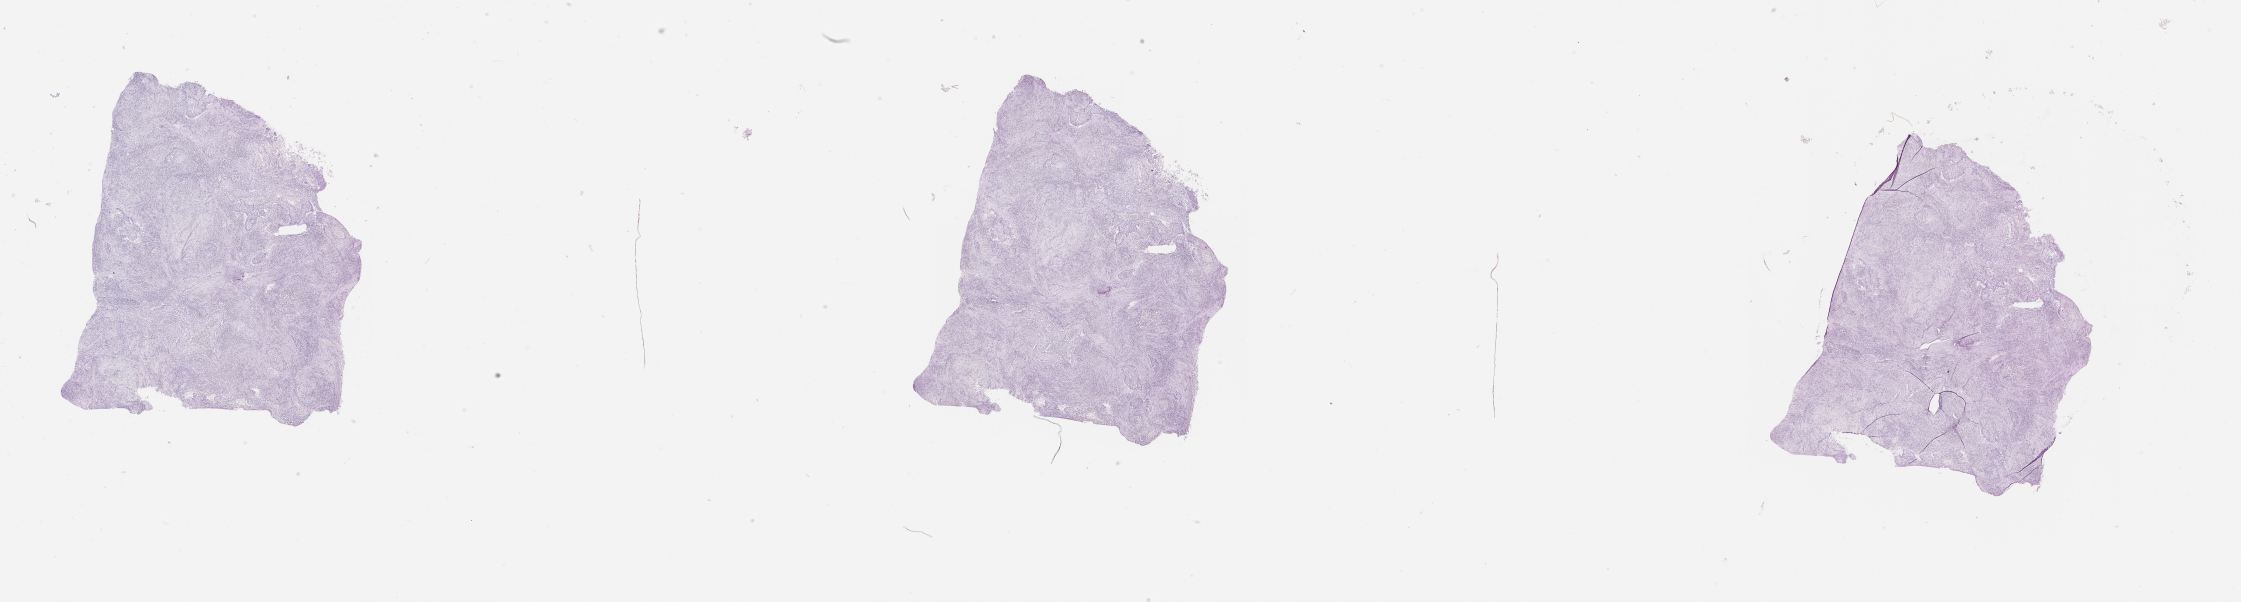
Hematoxylin and eosin (H&E) stained whole-slide image — whole scanned area (about 36.1 x 9.7 mm, acquisition: 20x scan) shown as a low-resolution overview; tumour tissue sample, lung. Male, 66 y/o.
Patient diagnosis (cohort enrolment): squamous cell carcinoma (lung).